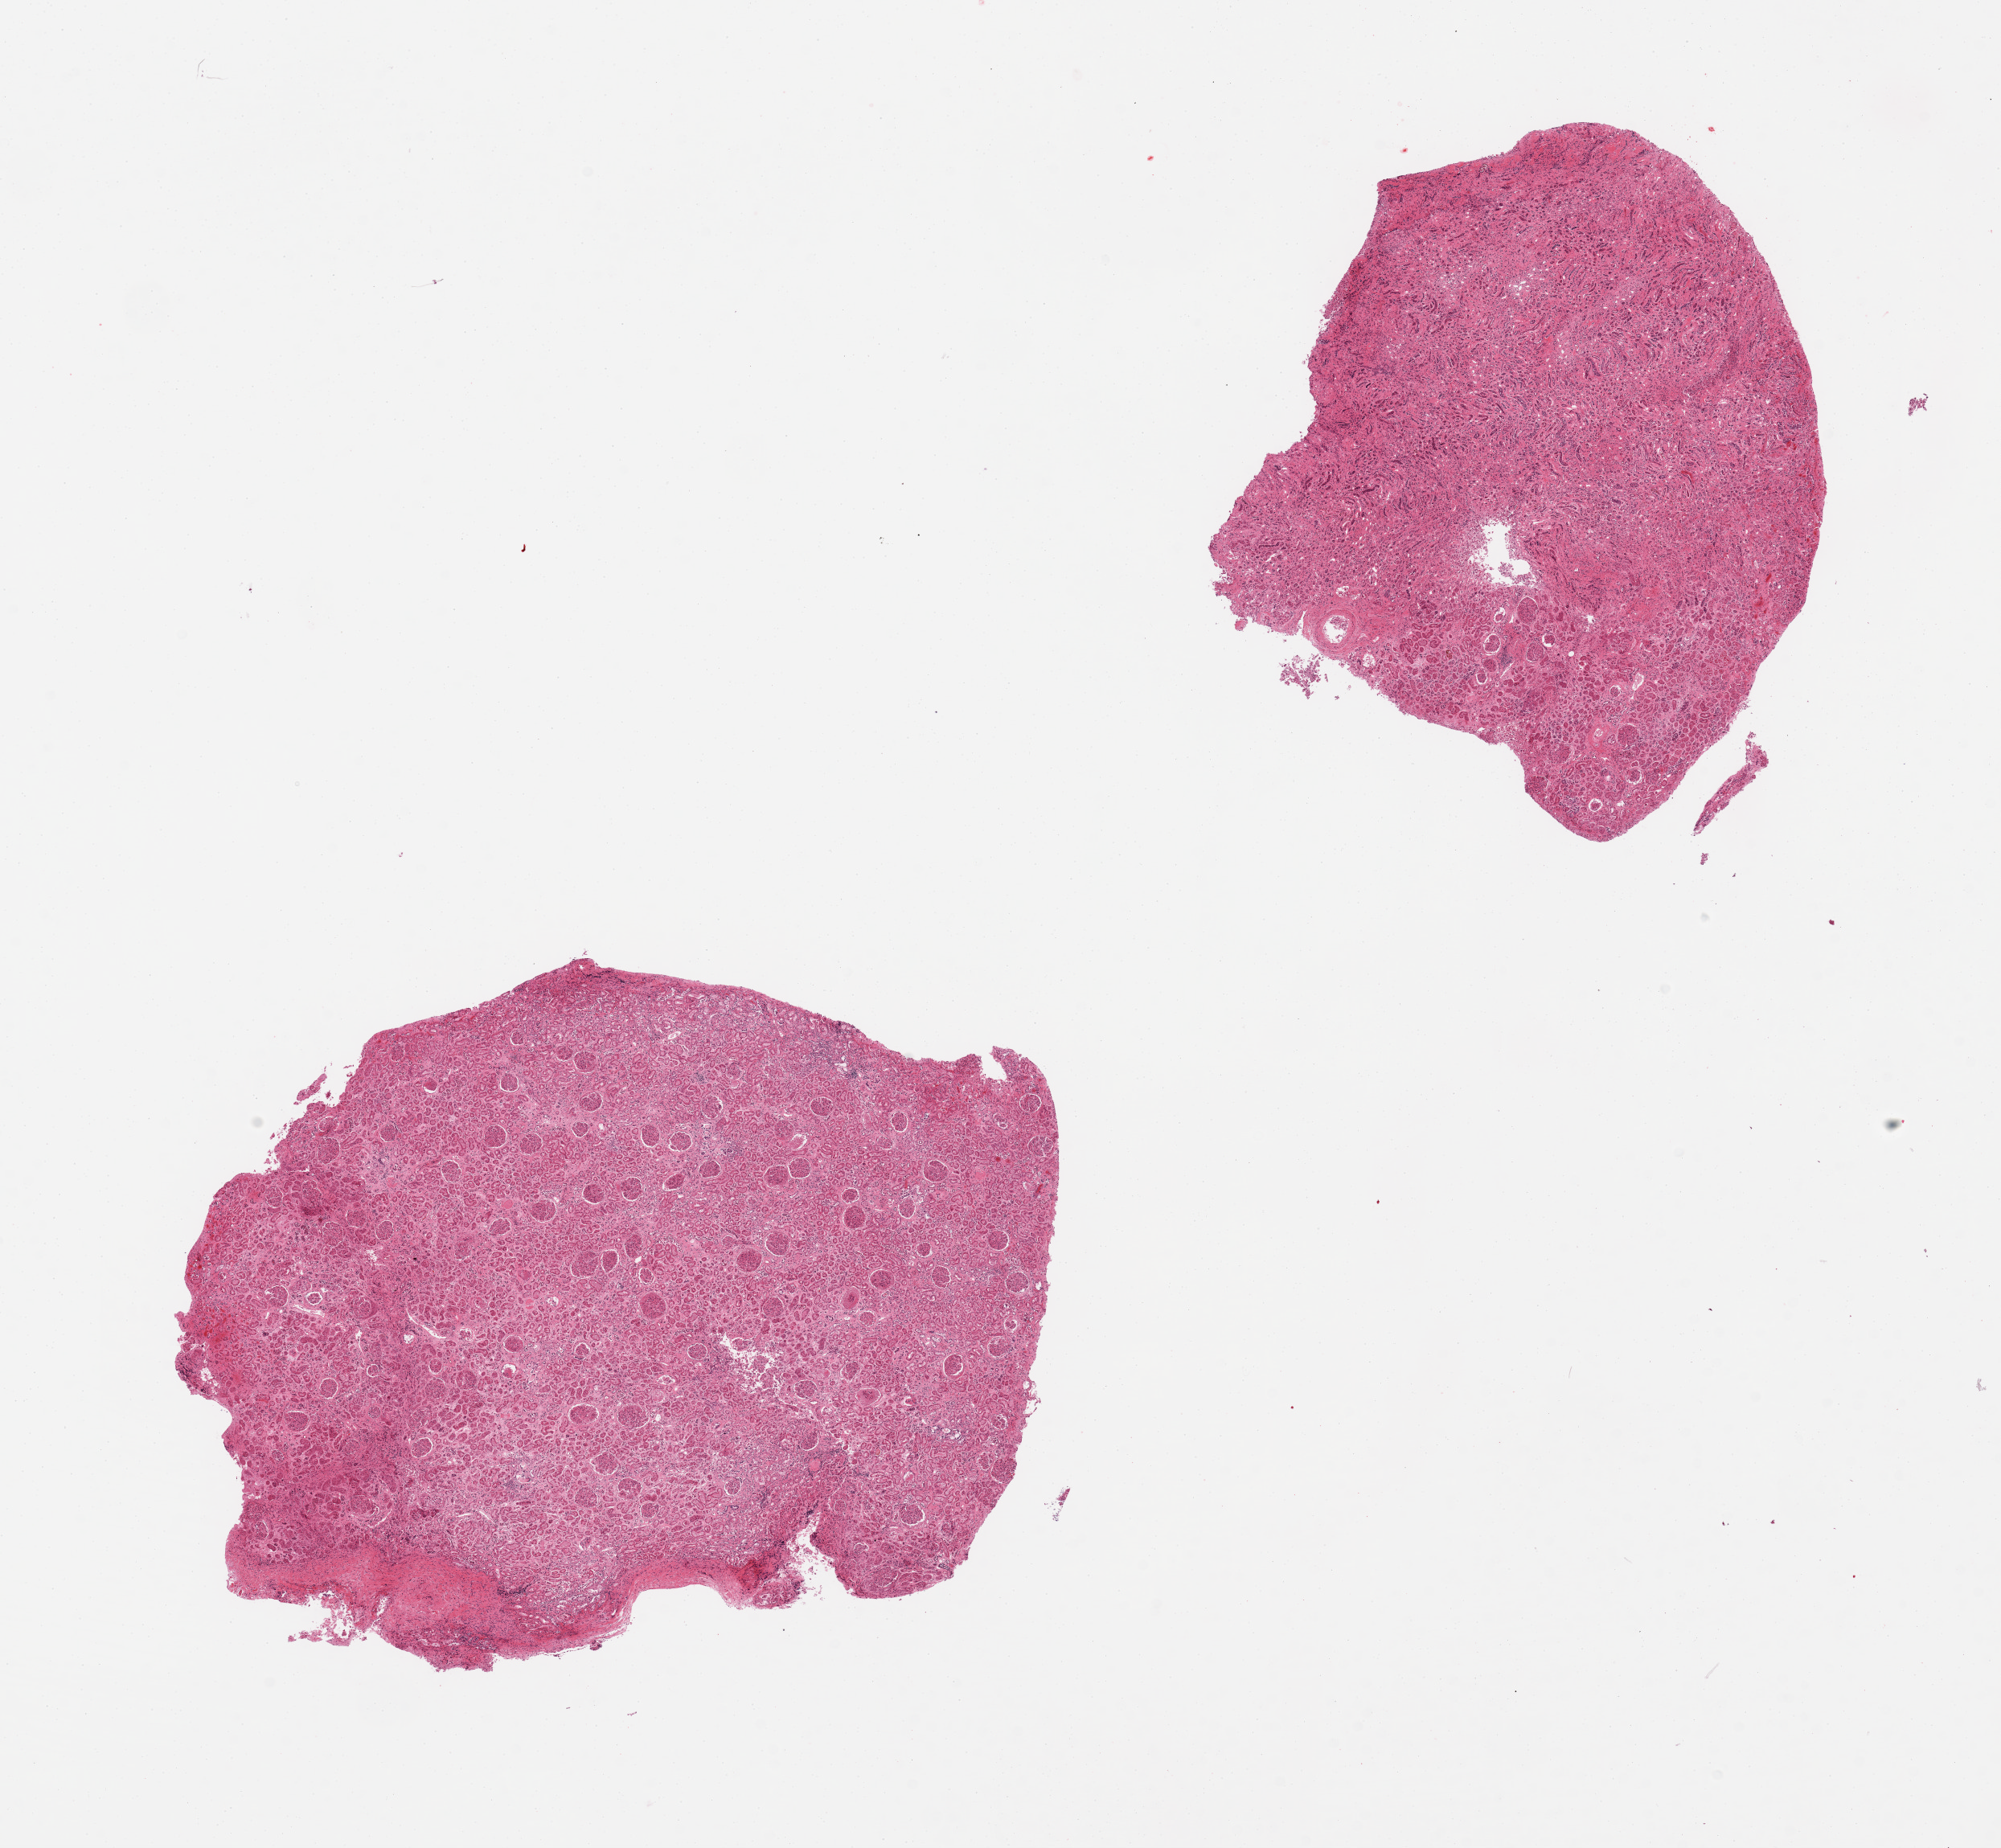
Whole-slide image, H&E stain — whole scanned area (about 19.7 x 18.2 mm, from a 20x scan) shown as a low-resolution overview, PAXgene-fixed, paraffin-embedded tissue, section of renal cortex (target tissue), tissue donor sample. Donor sex: female.
Pathologist's review note for this sample: 2 pieces, renal cortex/medulla, markedly autolyzed; no adrenal tissue present.